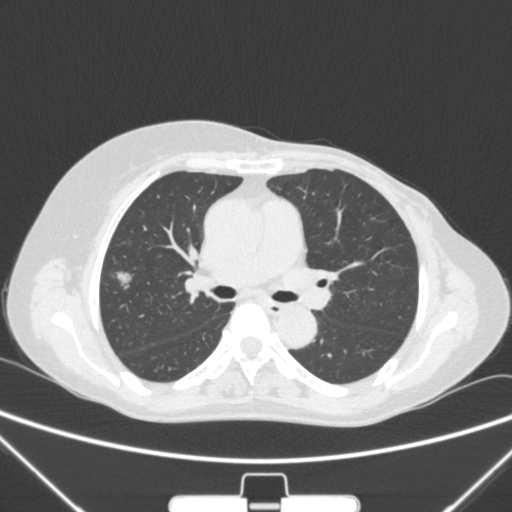
Chest CT, one axial slice; slice 153 of 265 in the series (ordered by position); 120 kVp; lung window (W 1500 / L -600 HU); 1 mm slice thickness; 512 × 512 image matrix, field of view 350 × 350 mm. Patient: female, 64 years. Case-level facts recorded for this patient, not image findings: clinical TNM (as recorded): T1c N0 M0; histopathological grade: G1-2.
Outlined on this slice (bounding box drawn by a radiologist):
- lung tumour (recorded histology: adenocarcinoma): bounding box <103,257,143,296> (left, top, right, bottom; pixels)